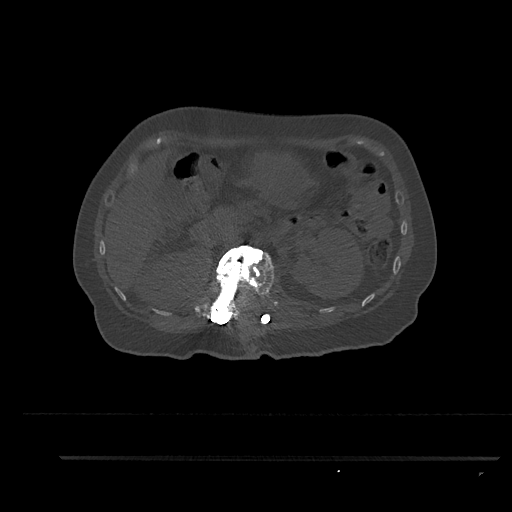
CT including the spine, one axial slice. Slice 222 of 797 in the series (ordered by position). Reconstruction kernel Br40s/3. 120 kVp. Bone window (W 1800 / L 400 HU). 0.5 mm slice thickness. 512 × 512 image matrix, field of view 408 × 408 mm. Patient: female, 44 years. Case-level facts recorded for this patient, not image findings: primary cancer: renal; vertebrae with lytic lesions (as recorded): L1.
Annotated regions visible in this slice (semi-automatic segmentation, software-assisted and operator-edited):
- L1 vertebra: bounding box <207,245,275,320> (left, top, right, bottom; pixels)